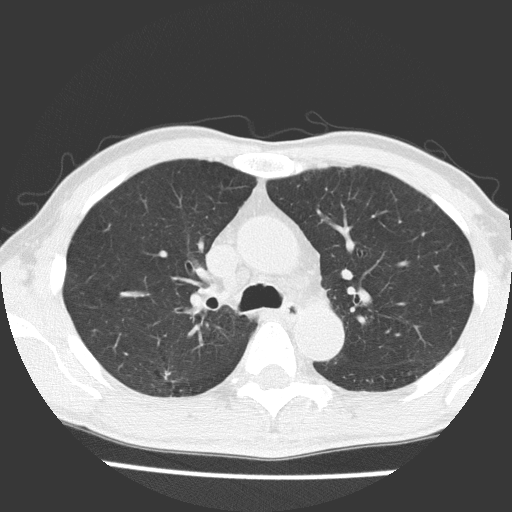
Low-dose screening chest CT, one axial slice; position 110 of 160 along the scan axis; reconstruction kernel FC51; 120 kVp; lung window (W 1500 / L -600 HU); 2 mm slice thickness; 512 × 512 image matrix, field of view 309 × 309 mm.
Structures marked on this image (manually delineated by an expert):
- lesion 1 (tumor, upper lobe of right lung): bounding box (x1, y1, x2, y2) in pixels: (164, 371, 172, 382)